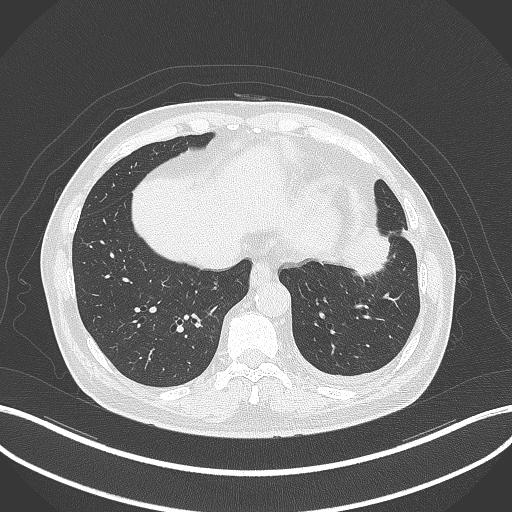
Chest CT, one axial slice; slice 91 of 230 in the series (ordered by position); reconstruction kernel B70f; 120 kVp; lung window (W 1500 / L -600 HU); 1 mm slice thickness; 512 × 512 image matrix, field of view 400 × 400 mm. Male patient, age 68 years. Case-level facts recorded for this patient, not image findings: clinical TNM (as recorded): T2b N0 M0.
Annotated regions visible in this slice (bounding box drawn by a radiologist):
- lung tumour (recorded histology: squamous cell carcinoma): bounding box <342,220,392,278> (left, top, right, bottom; pixels)